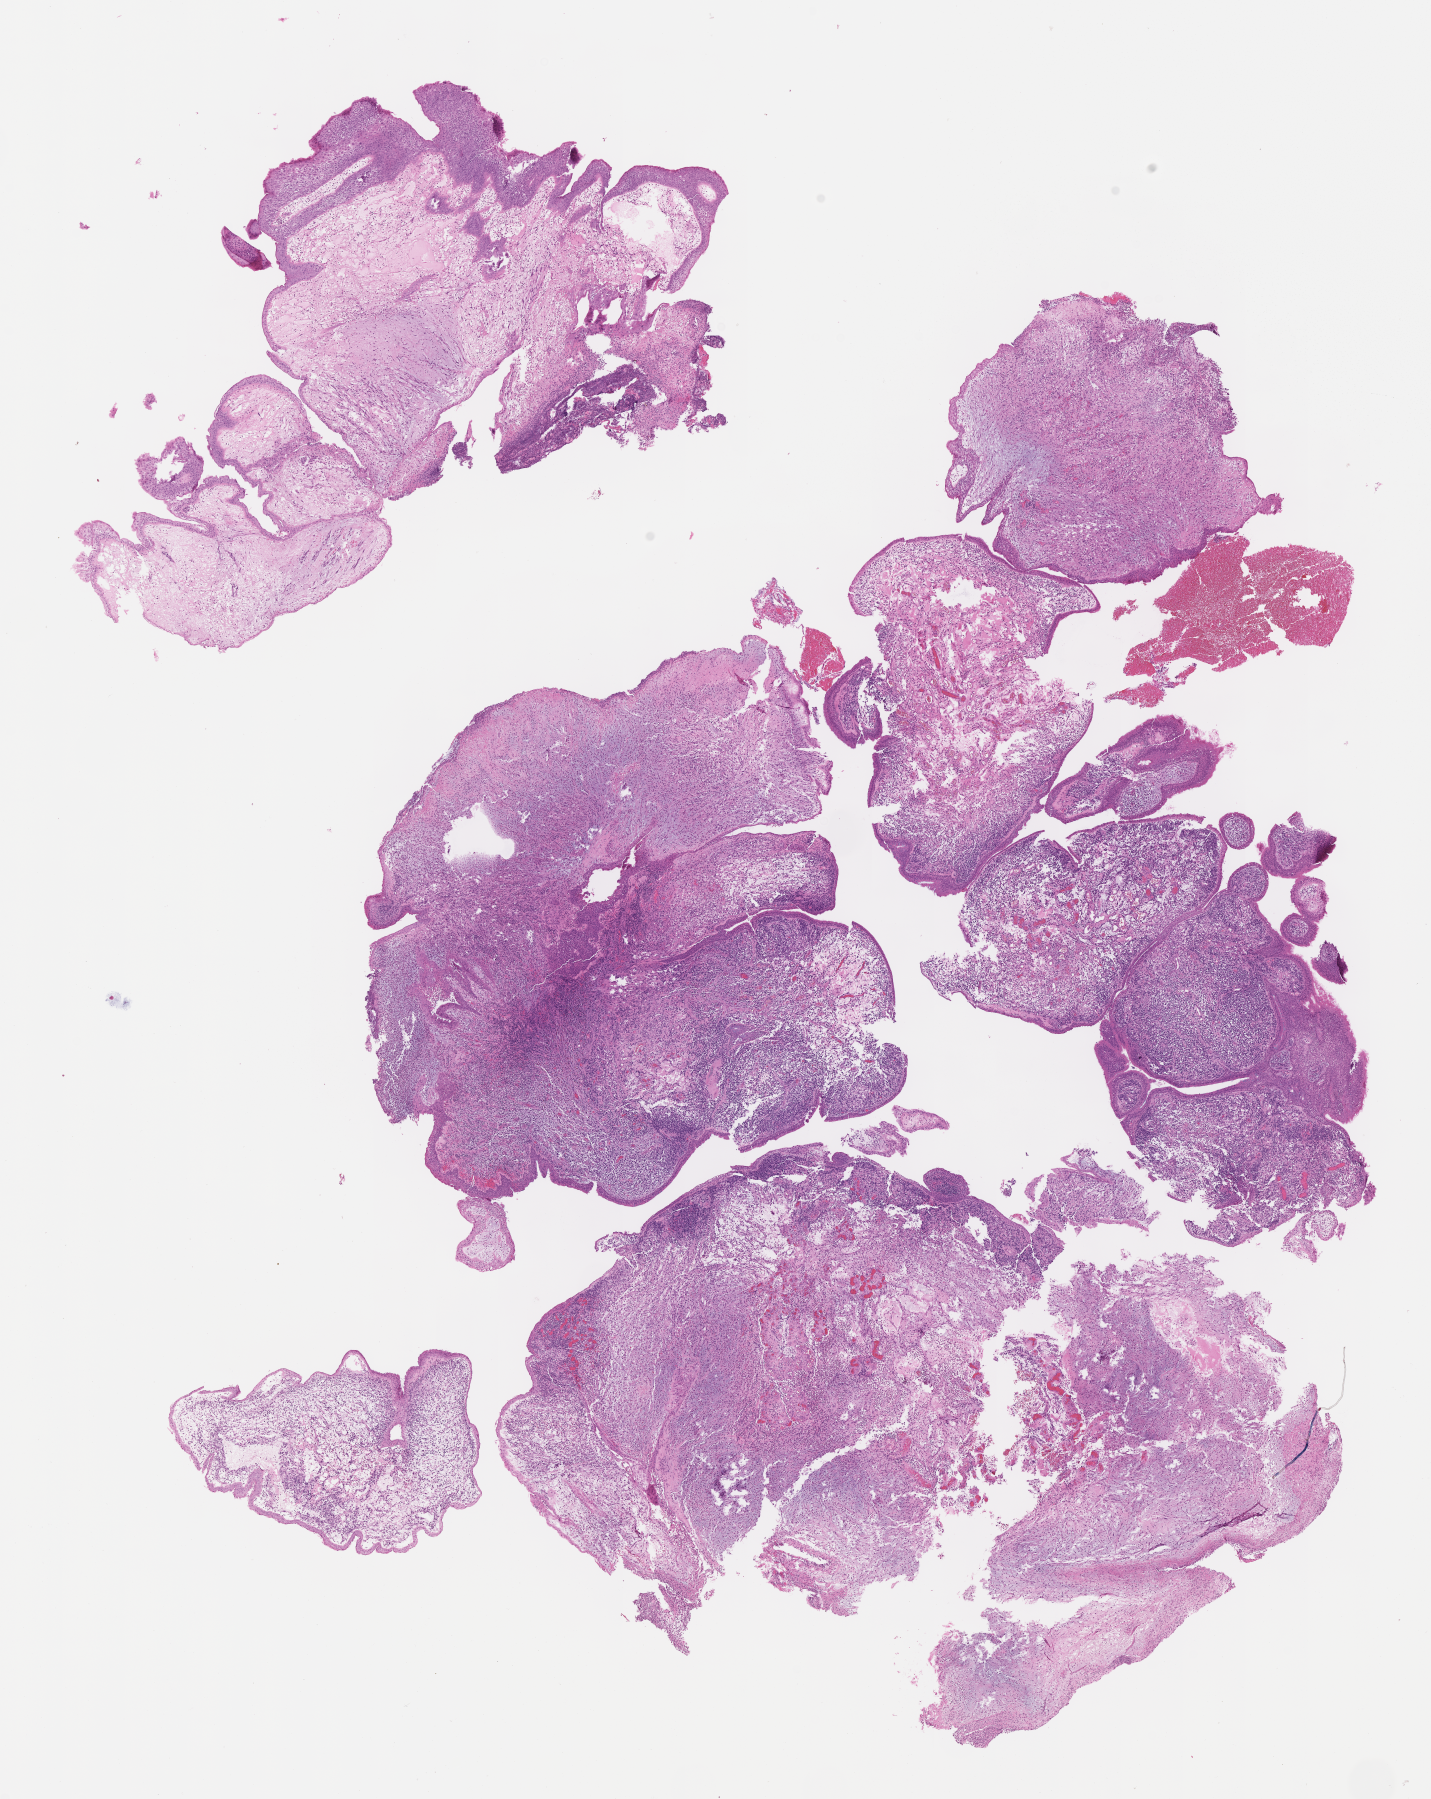
Whole-slide image, hematoxylin and eosin (H&E) stain of tumor tissue — a low-resolution overview of the entire scanned area, about 11.6 x 14.5 mm, FFPE section, site: oral Dorsal soft palate. Female patient, age at diagnosis 7.1 years.
Metastatic status at presentation (as recorded): non-metastatic (confirmed). Stage (as recorded): 3. Diagnosis: rhabdomyosarcoma; histological classification: embryonal rhabdomyosarcoma.